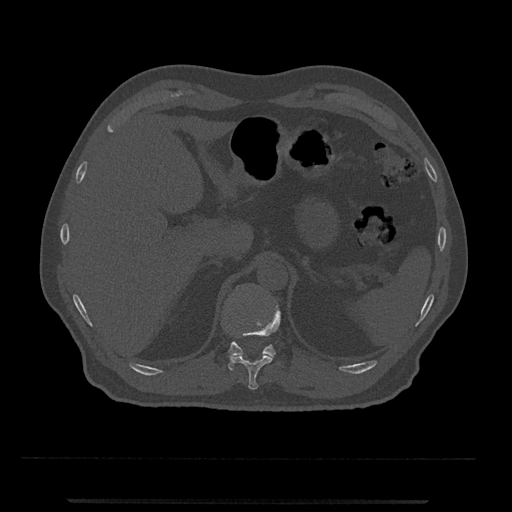
CT including the spine, one axial slice; slice 438 of 797 in the series (ordered by position); reconstruction kernel Br40s/3; bone window (W 1800 / L 400 HU); 0.5 mm slice thickness; 512 × 512 image matrix. Patient: male, 63 years. Case-level facts recorded for this patient, not image findings: primary cancer: prostate.
Annotated regions visible in this slice (semi-automatic segmentation, software-assisted and operator-edited):
- T11 vertebra: bounding box [x1, y1, x2, y2] px = [230, 306, 281, 390]
- T12 vertebra: [226, 286, 276, 371]